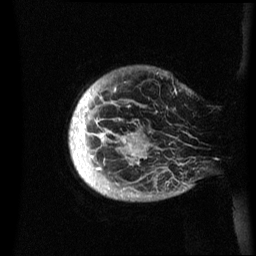
Breast MRI (dynamic contrast-enhanced), one sagittal slice. Position 3 of 60 along the scan axis. Dynamic contrast-enhanced series, image 2 of 3 at this slice position (ordered by acquisition). 1.5 T. TE 4.2 ms, TR 8.4 ms. 256 × 256 image matrix, field of view 230 × 230 mm. Female patient, age 48 years.
Structures marked on this image (semi-automatic segmentation, software-assisted and operator-edited):
- analysis volume of interest (the breast-tissue region the enhancement analysis was run in; not a lesion): bounding box <69,66,199,202> (left, top, right, bottom; pixels)
- tumour enhancement mask (voxels above the 70 % enhancement threshold inside the analysis volume of interest): <71,87,146,170>